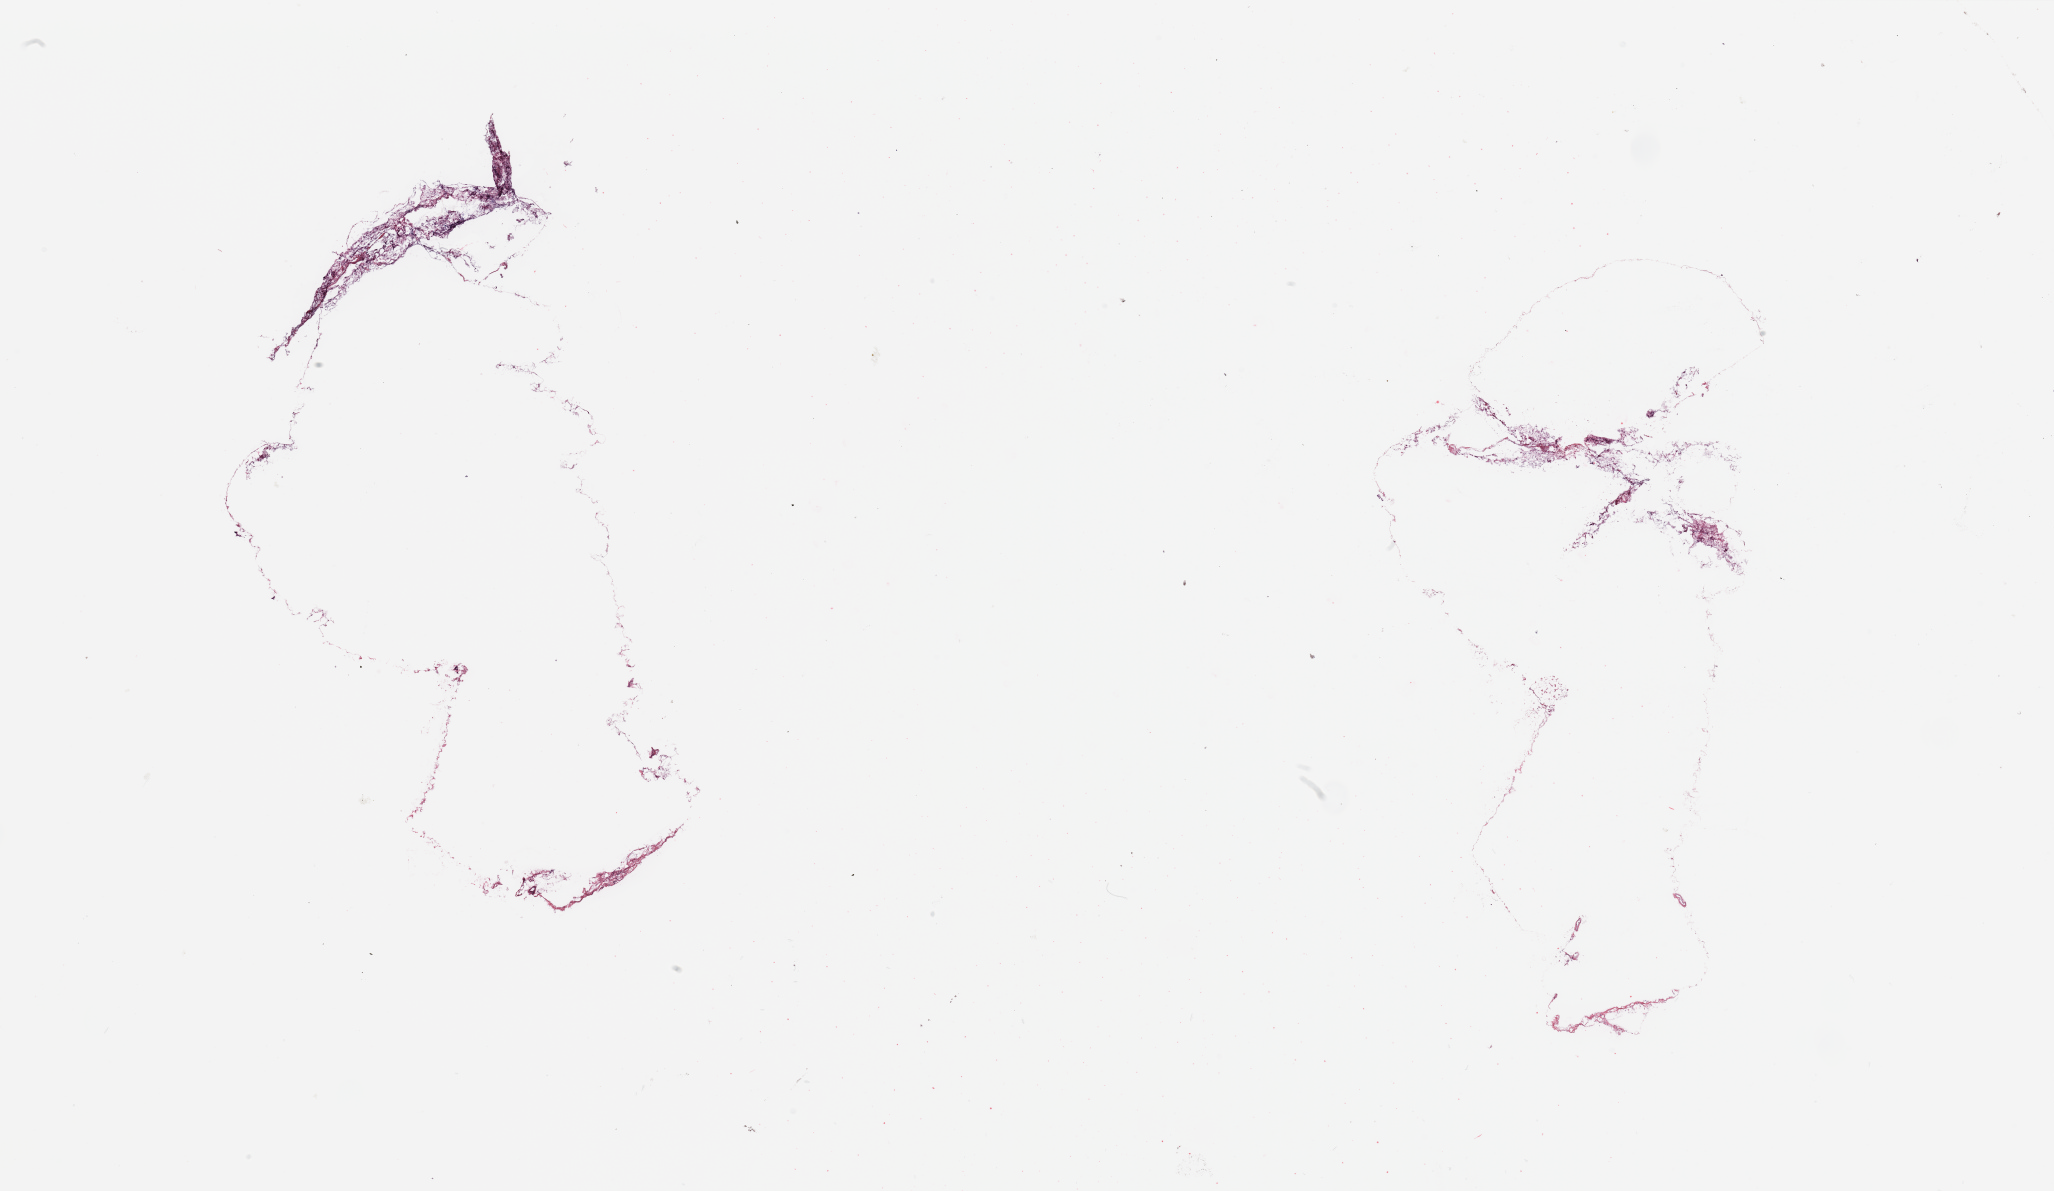
Digitized H&E tissue section (whole slide), shown as a low-resolution overview of the whole scanned area (about 32.5 x 18.8 mm, acquisition: 20x scan); breast, tumour tissue. Female, 71 y/o.
• AJCC pathologic stage: IIIB
• histologic diagnosis: Intraductal papillary carcinoma